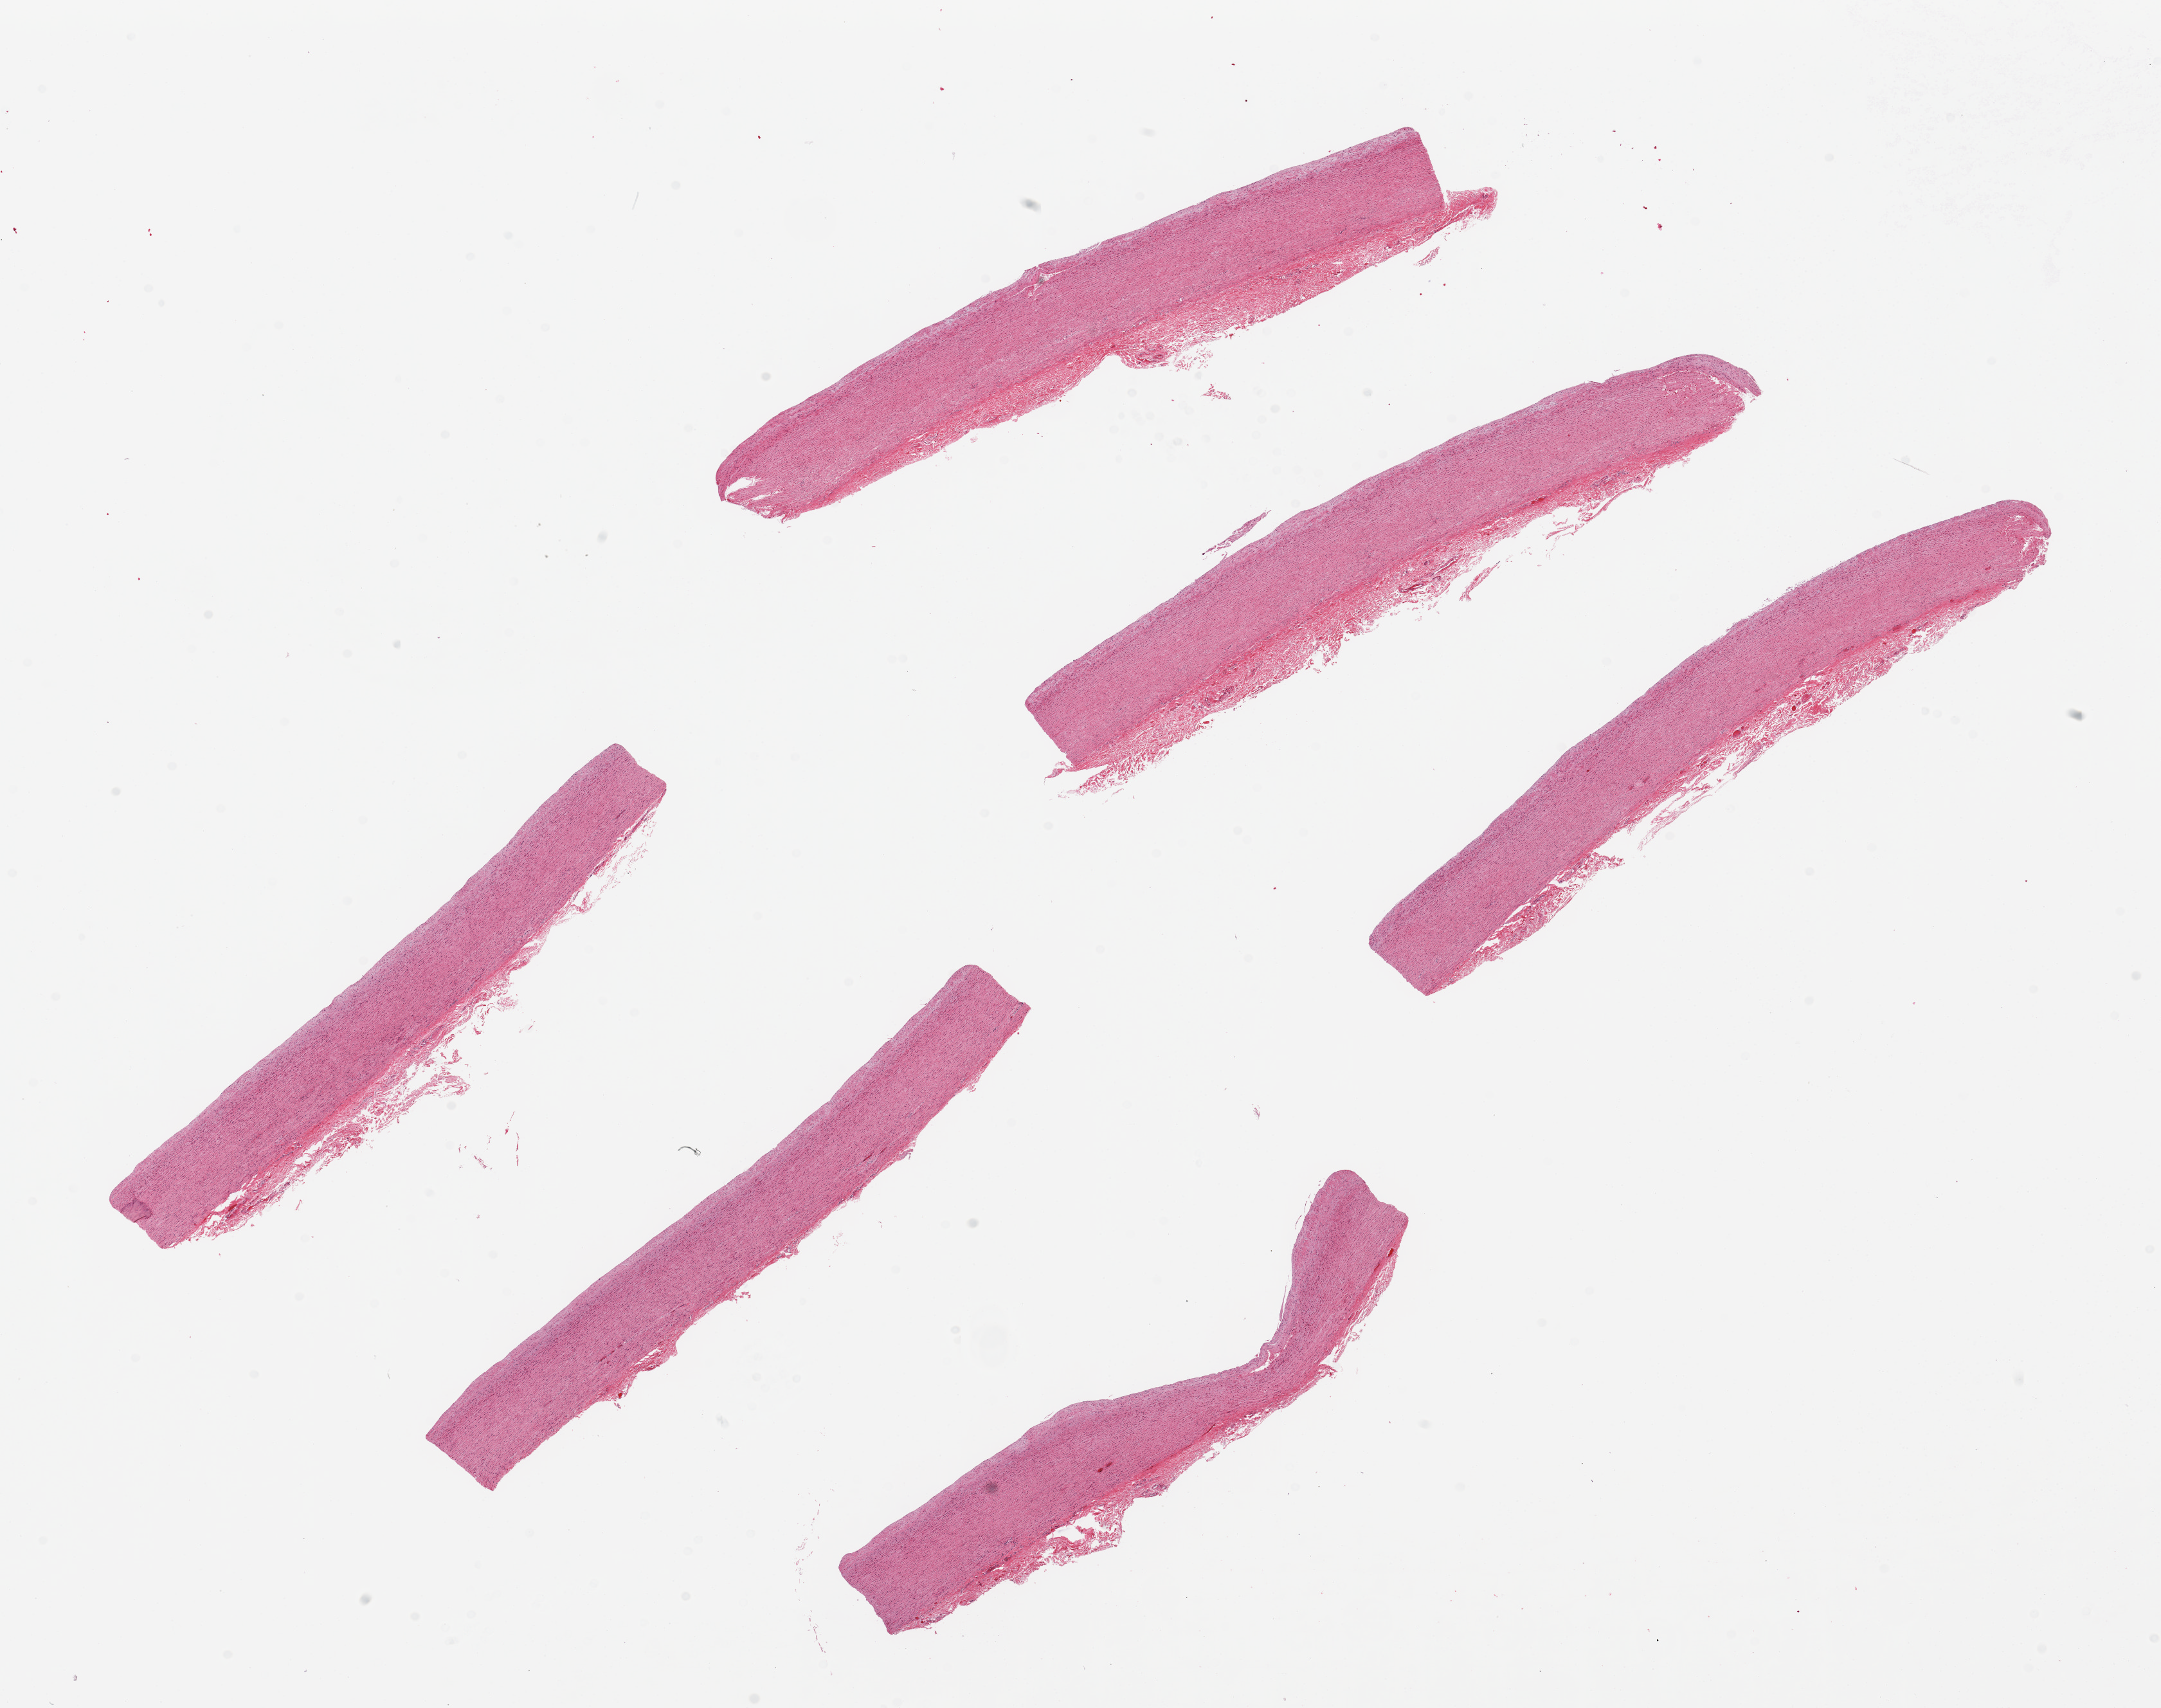
Hematoxylin and eosin (H&E) whole-slide image, a low-resolution overview of the entire scanned area, about 26.6 x 21.0 mm; PAXgene-fixed paraffin-embedded (PFPE) section; target tissue: aorta; tissue donor sample. Donor sex: male.
Review note (as recorded): 6 pieces up to 9.6x1.7 mm.